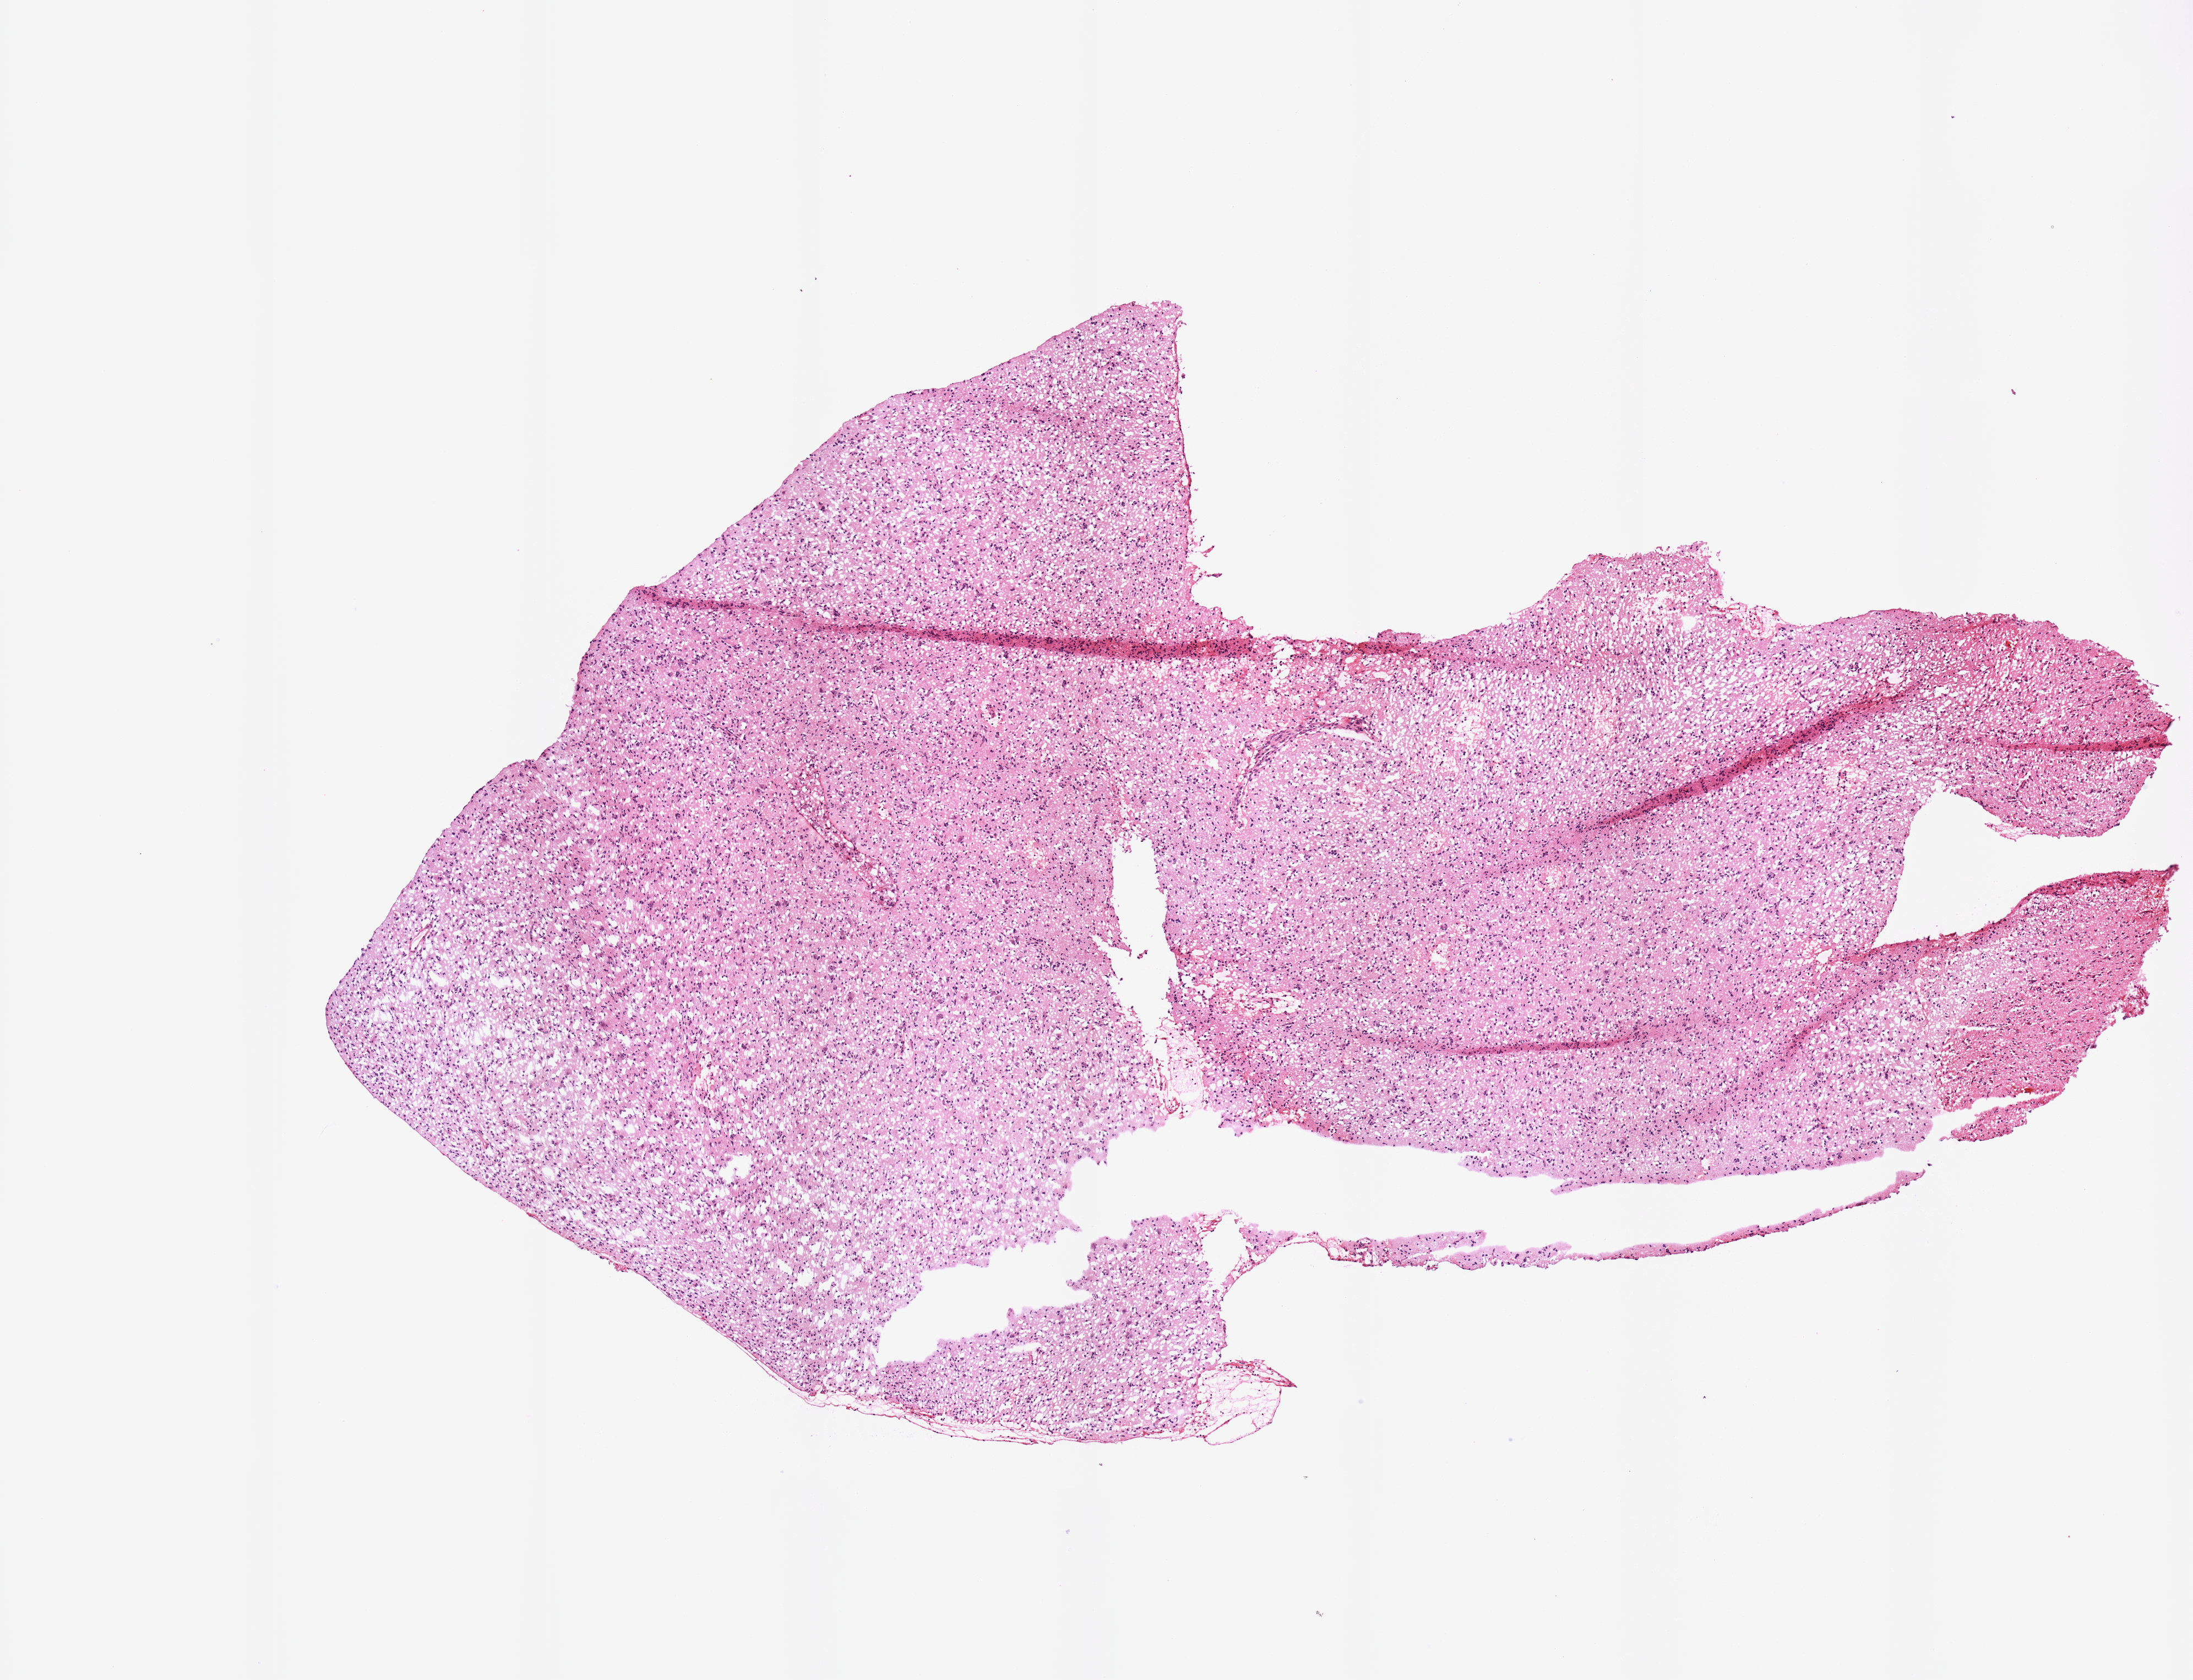
Hematoxylin and eosin (H&E) stained whole-slide image, shown as a low-resolution overview of the whole scanned area (about 7.9 x 6.0 mm, slide scanned at 20x). Brain, tumour tissue. Patient: male, age 65 years.
* primary tumour site (as recorded): left hemisphere
* patient diagnosis (cohort enrolment): glioblastoma multiforme (brain)